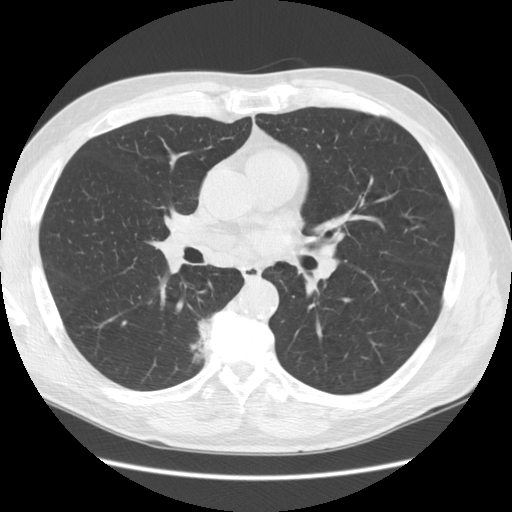
Low-dose screening chest CT, one axial slice; slice 71 of 133 in the series (ordered by position); reconstruction kernel STANDARD; 120 kVp; lung window (W 1500 / L -600 HU); 512 × 512 image matrix.
Outlined on this slice (outlined manually by an expert reader):
- lesion 1 (tumor, lower lobe of right lung): box from (x=191, y=317) to (x=212, y=363) px